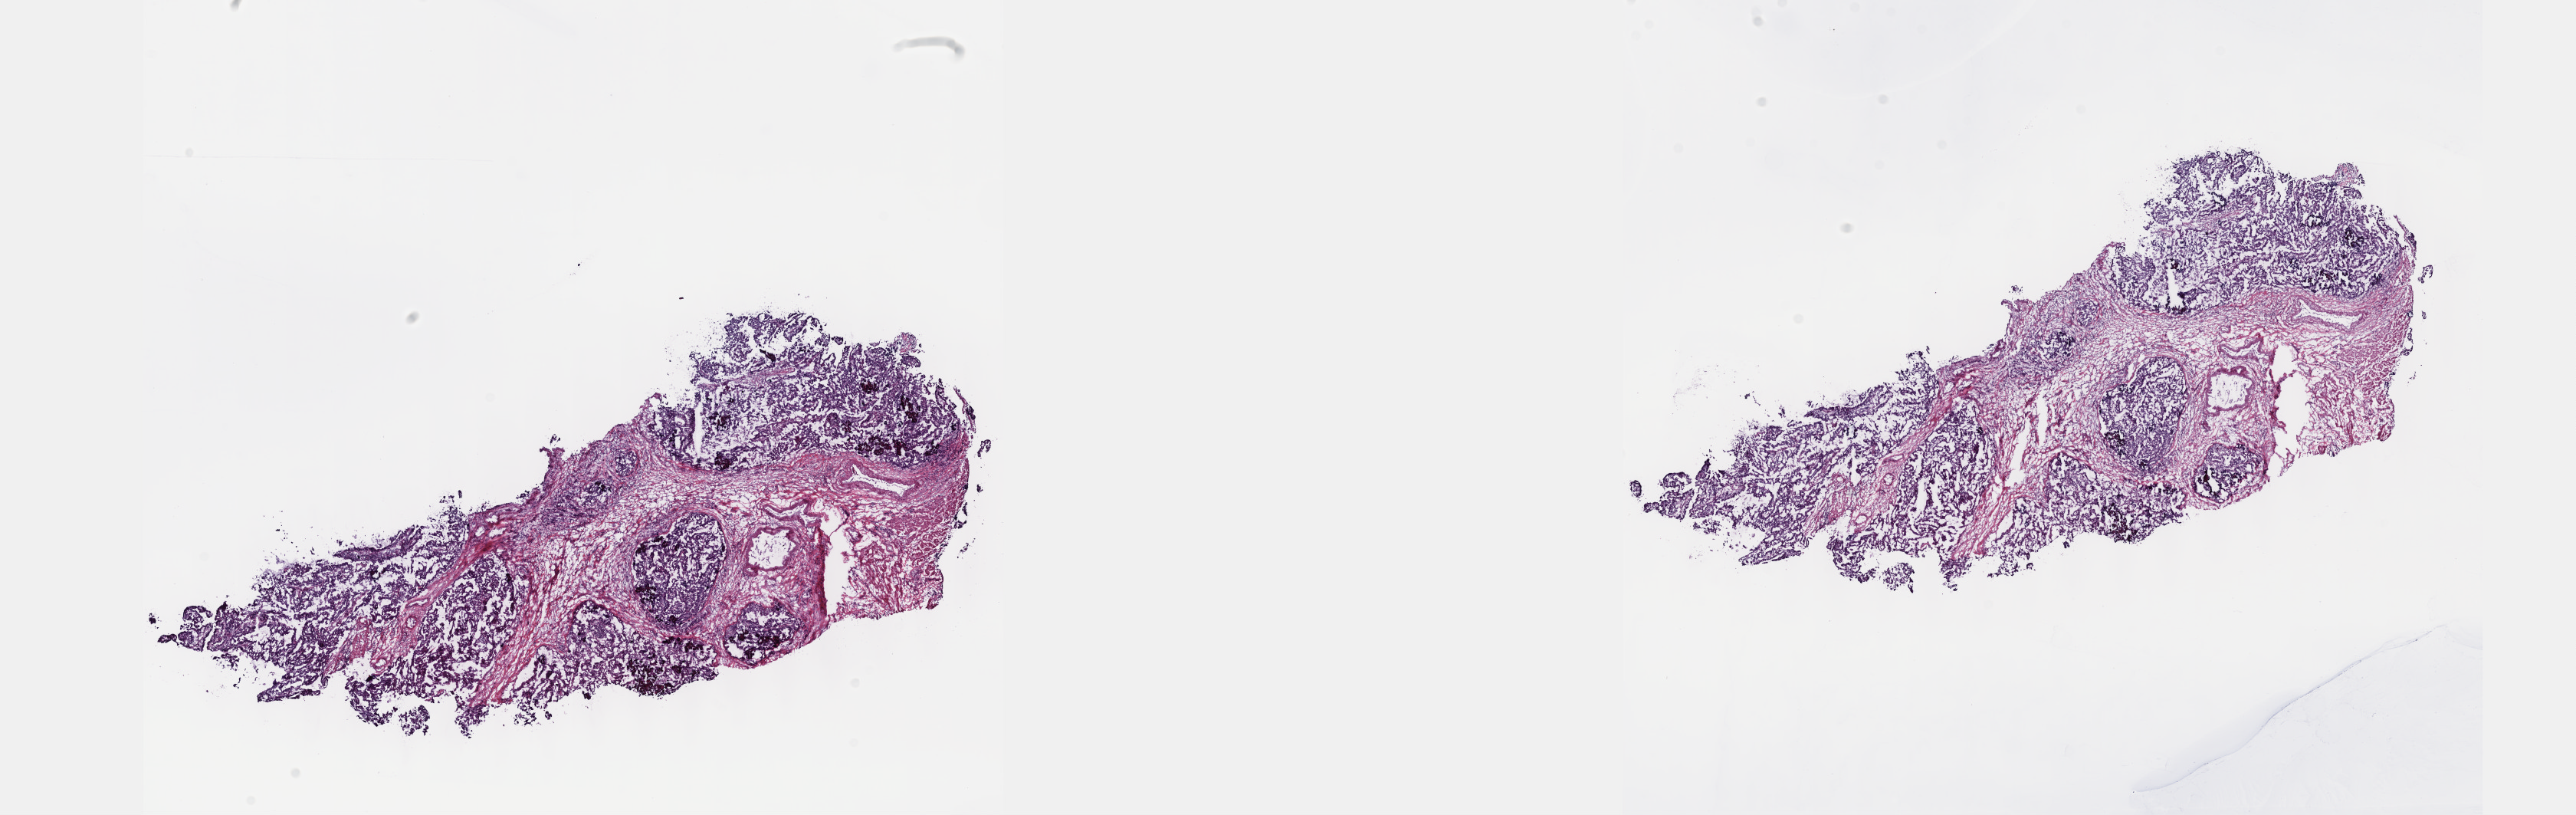
Digitized H&E tissue section (whole slide), low-resolution overview of the scanned area, about 27.2 x 8.6 mm. Frozen section. Sample: primary tumour, esophagus. Male, age 67 years at initial diagnosis. Histologic grade: G3 (poorly differentiated). Pathologist review of this section (percent, as recorded): tumour cells 50%, tumour nuclei 60%, normal cells 0%, stromal cells 50%, necrosis 0%. Infiltration values recorded for this section: lymphocyte infiltration 0%, monocyte infiltration 0%, neutrophil infiltration 0%.
TNM: T3 N1 M0. Histologic diagnosis: Adenocarcinoma, NOS (lower third of esophagus). AJCC pathologic stage: III (5th edition). Lymph nodes positive (case pathology): 7 of 8 examined.